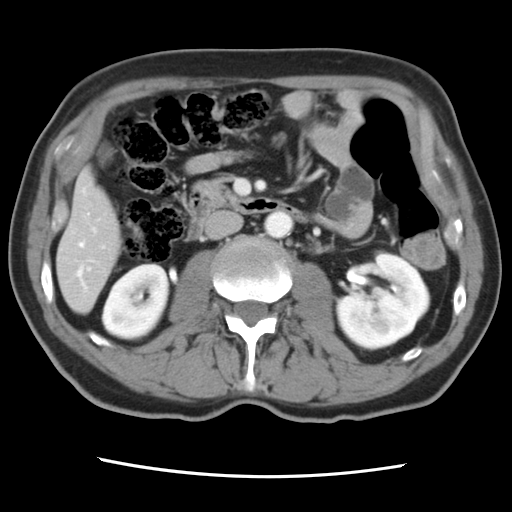
Contrast-enhanced abdominal CT, one axial slice. Position 27 of 83 along the scan axis. 120 kVp. Intravenous contrast given. Soft-tissue window (W 400 / L 40 HU). 512 × 512 image matrix, field of view 321 × 321 mm. Male patient, age 69 years. Case-level facts recorded for this patient, not image findings: diagnosis: colorectal cancer liver metastases, imaged before liver resection; multiple liver metastases: yes; largest metastasis: 3.5 cm; disease in both lobes: no.
Outlined on this slice (expert manual segmentation):
- hepatic veins: box from (x=77, y=243) to (x=85, y=286) px
- liver: (x=58, y=173)–(x=120, y=312)
- planned liver remnant (the part of the liver to remain after resection): (x=58, y=172)–(x=121, y=312)